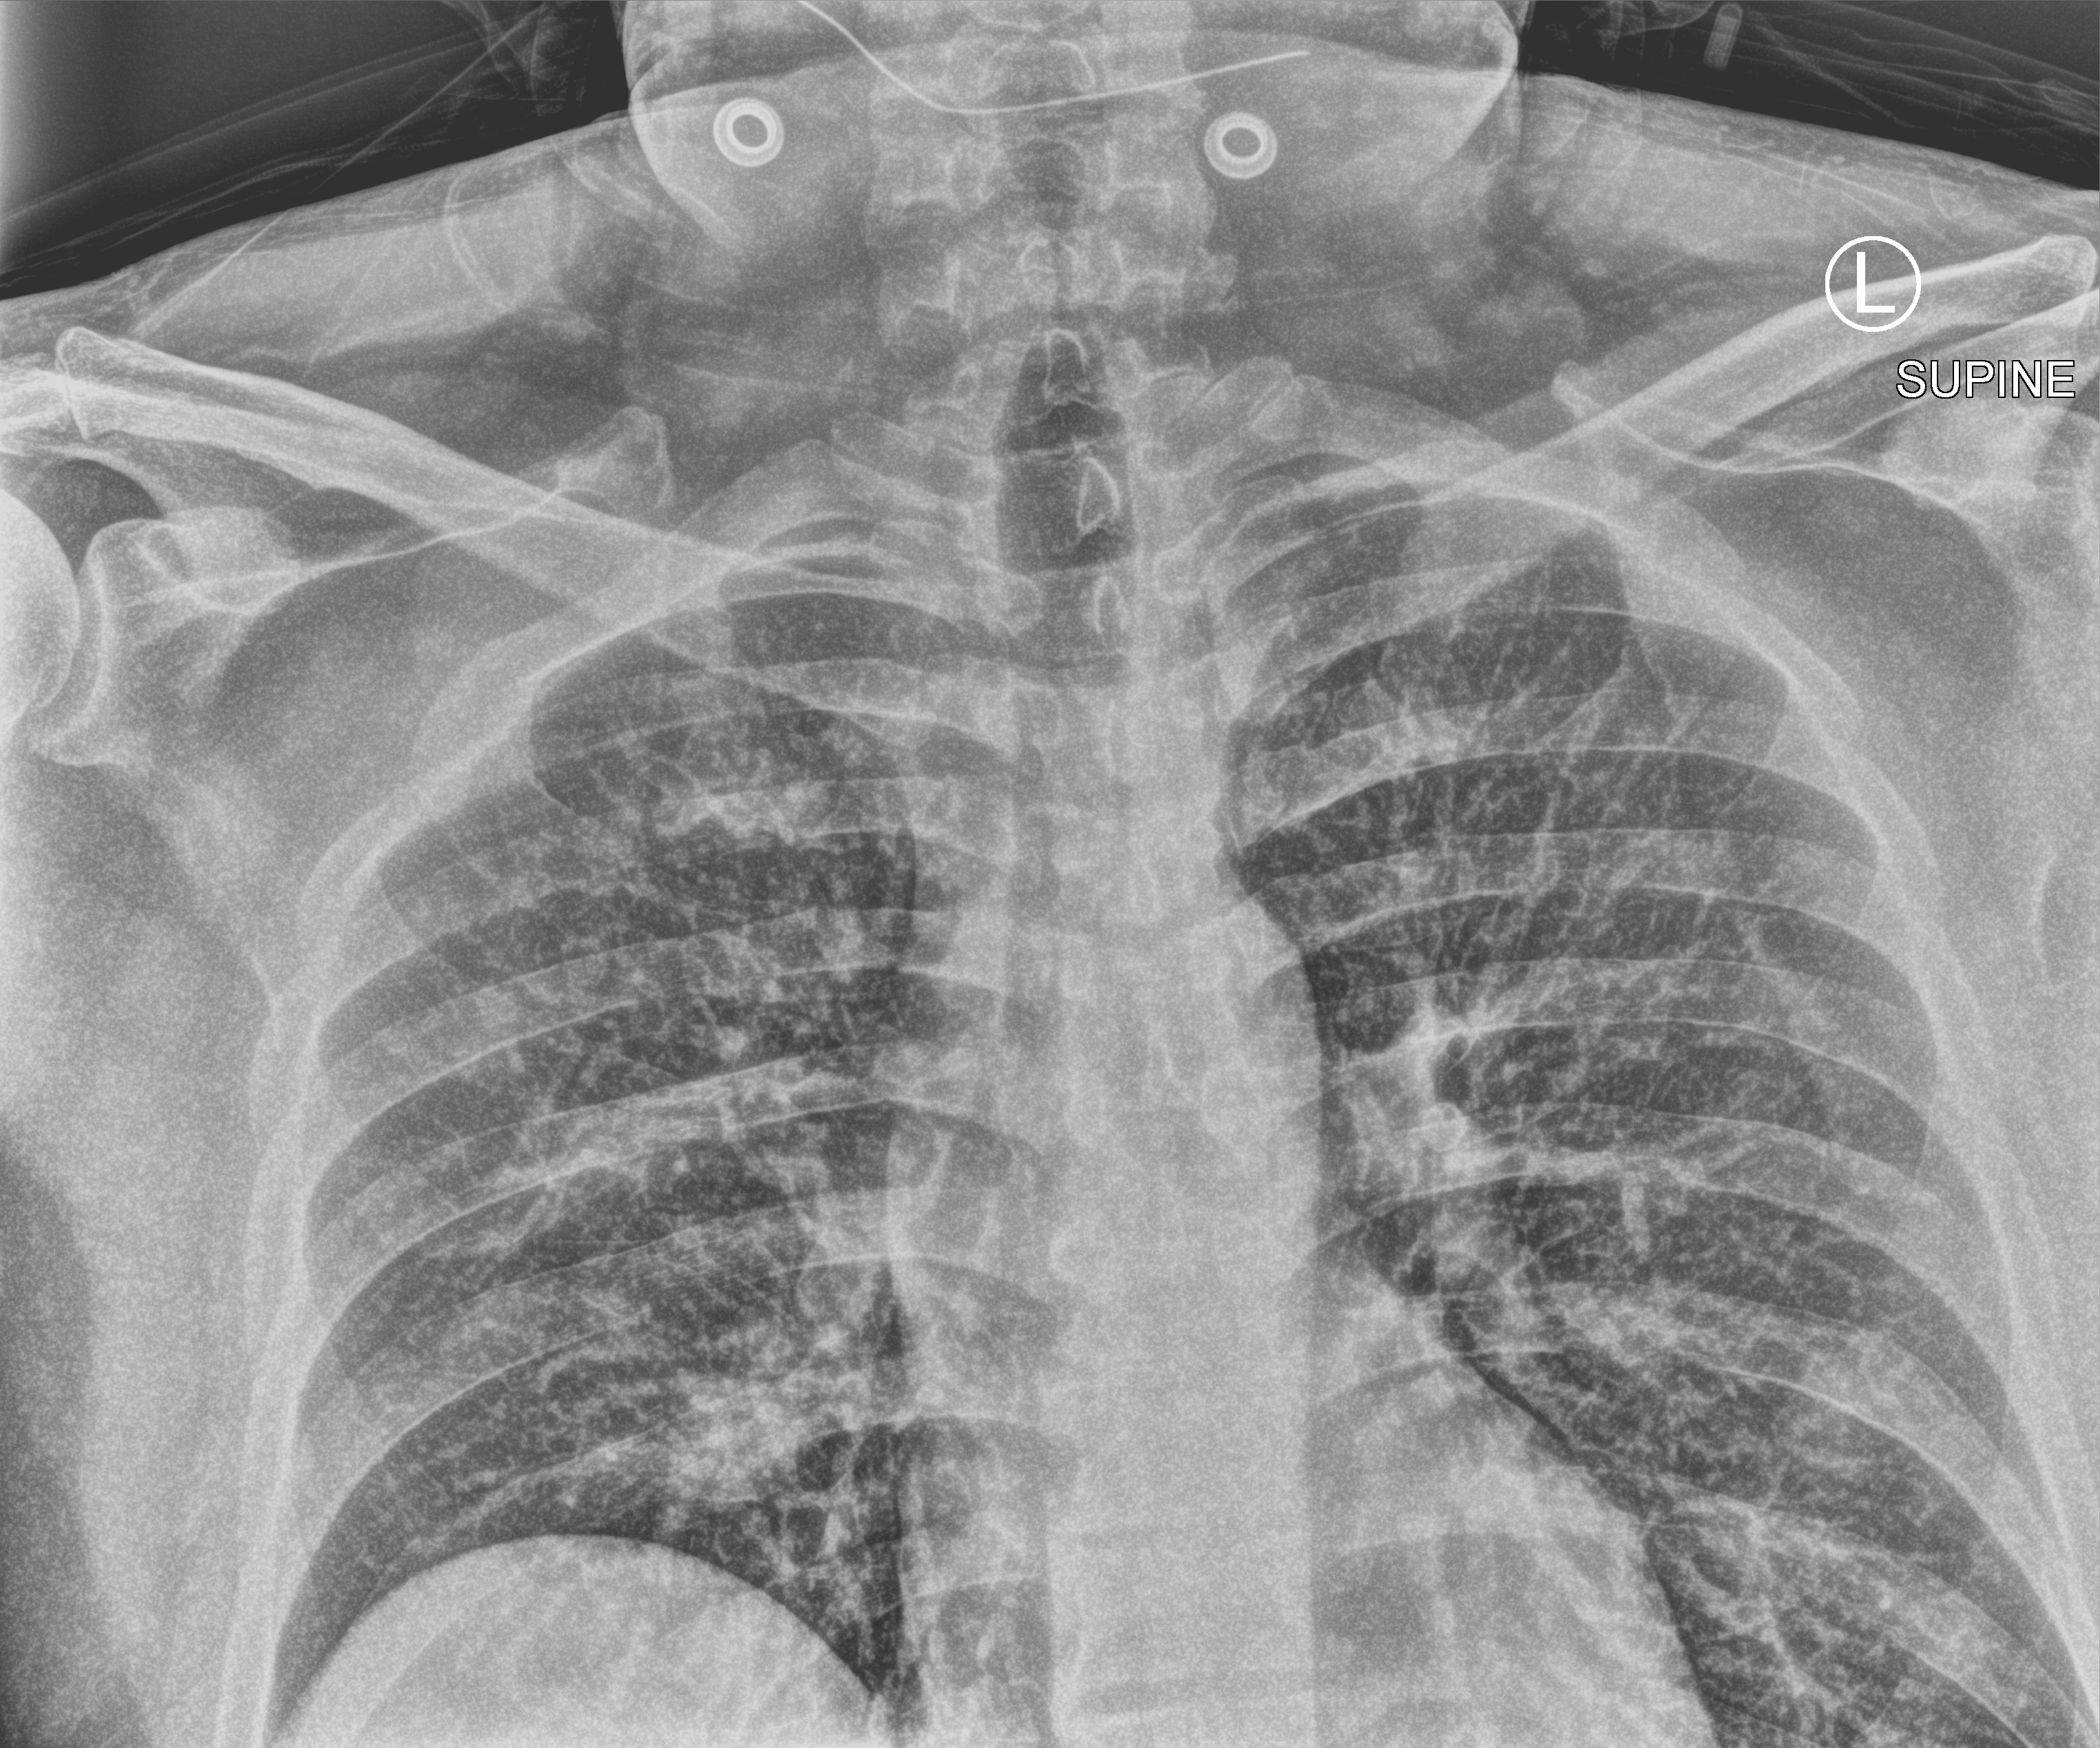
Chest X-ray (portable); anteroposterior (AP) projection. Male patient hospitalised with COVID-19, age 18–59 years.
From the hospital-stay record, not from the radiograph (when in the stay this image was taken is not recorded): mechanically ventilated during this hospital stay: no; length of hospital stay: 2 days; admitted to intensive care during this hospital stay: no.